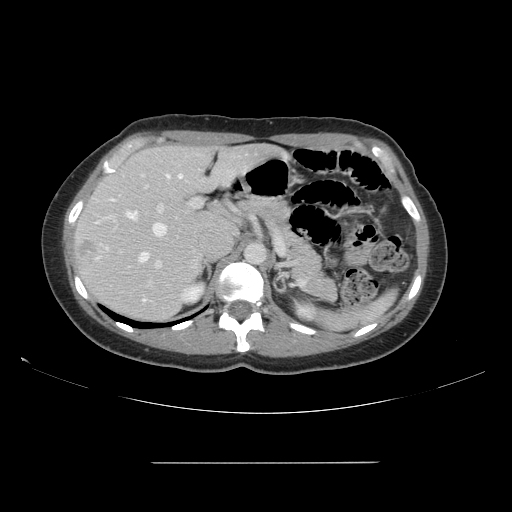
Contrast-enhanced abdominal CT, one axial slice; slice 101 of 151 in the series (ordered by position); 120 kVp; soft-tissue window (W 400 / L 40 HU); 512 × 512 image matrix. Female patient, age 46 years. From the clinical record (not read from this slice): diagnosis: colorectal cancer liver metastases, imaged before liver resection; multiple liver metastases: yes; largest metastasis: 3 cm; chemotherapy before resection: no.
Structures marked on this image (manually delineated by an expert):
- hepatic veins: bounding box <95,174,183,263> (left, top, right, bottom; pixels)
- liver: <74,145,275,322>
- planned liver remnant (the part of the liver to remain after resection): <89,147,278,255>
- portal vein (with intrahepatic branches): <141,174,202,302>
- liver metastasis: <79,241,97,258>